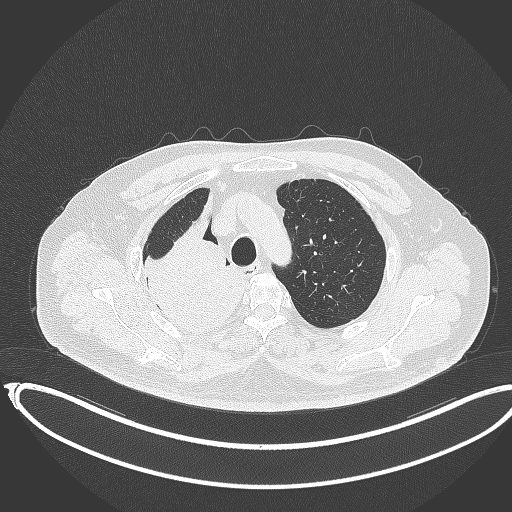
Chest CT, one axial slice; slice 289 of 403 in the series (ordered by position); lung window (W 1500 / L -600 HU); 512 × 512 image matrix, field of view 436 × 436 mm. Patient: male, 68 years. From the clinical record (not read from this slice): clinical TNM (as recorded): T2a N0 M0.
Structures marked on this image (rectangle marked by the reading radiologist):
- lung tumour (recorded histology: adenocarcinoma): bounding box [x1, y1, x2, y2] px = [137, 194, 251, 340]